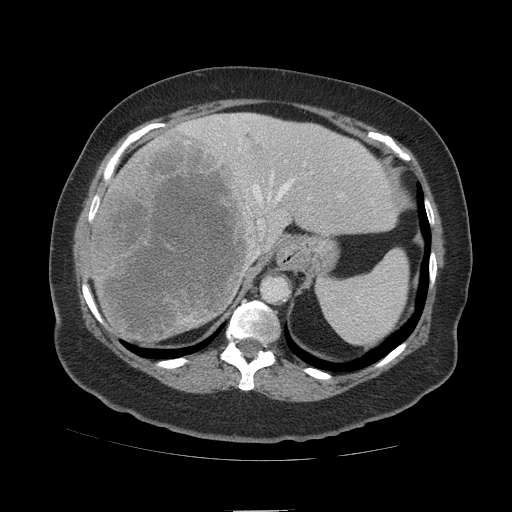
Contrast-enhanced abdominal CT (liver protocol), one axial slice. Position 81 of 109 along the scan axis. 140 kVp. Soft-tissue window (W 400 / L 40 HU). 512 × 512 image matrix. From the clinical record (not read from this slice): diagnosis: hepatocellular carcinoma (patient treated with transarterial chemoembolisation; whether this scan precedes or follows treatment is not stated here); TNM stage (as recorded): Stage-IVB; Child-Pugh class: A; tumour differentiation: poorly differentiated; tumour nodularity: multinodular.
Outlined on this slice (semi-automatic segmentation, software-assisted and operator-edited):
- liver parenchyma outside the tumour (the mass and vessels are separate outlines, so this box may not span the whole liver): bounding box [x1, y1, x2, y2] px = [84, 112, 396, 340]
- mass: [92, 129, 269, 341]
- liver vessels: [96, 114, 340, 258]